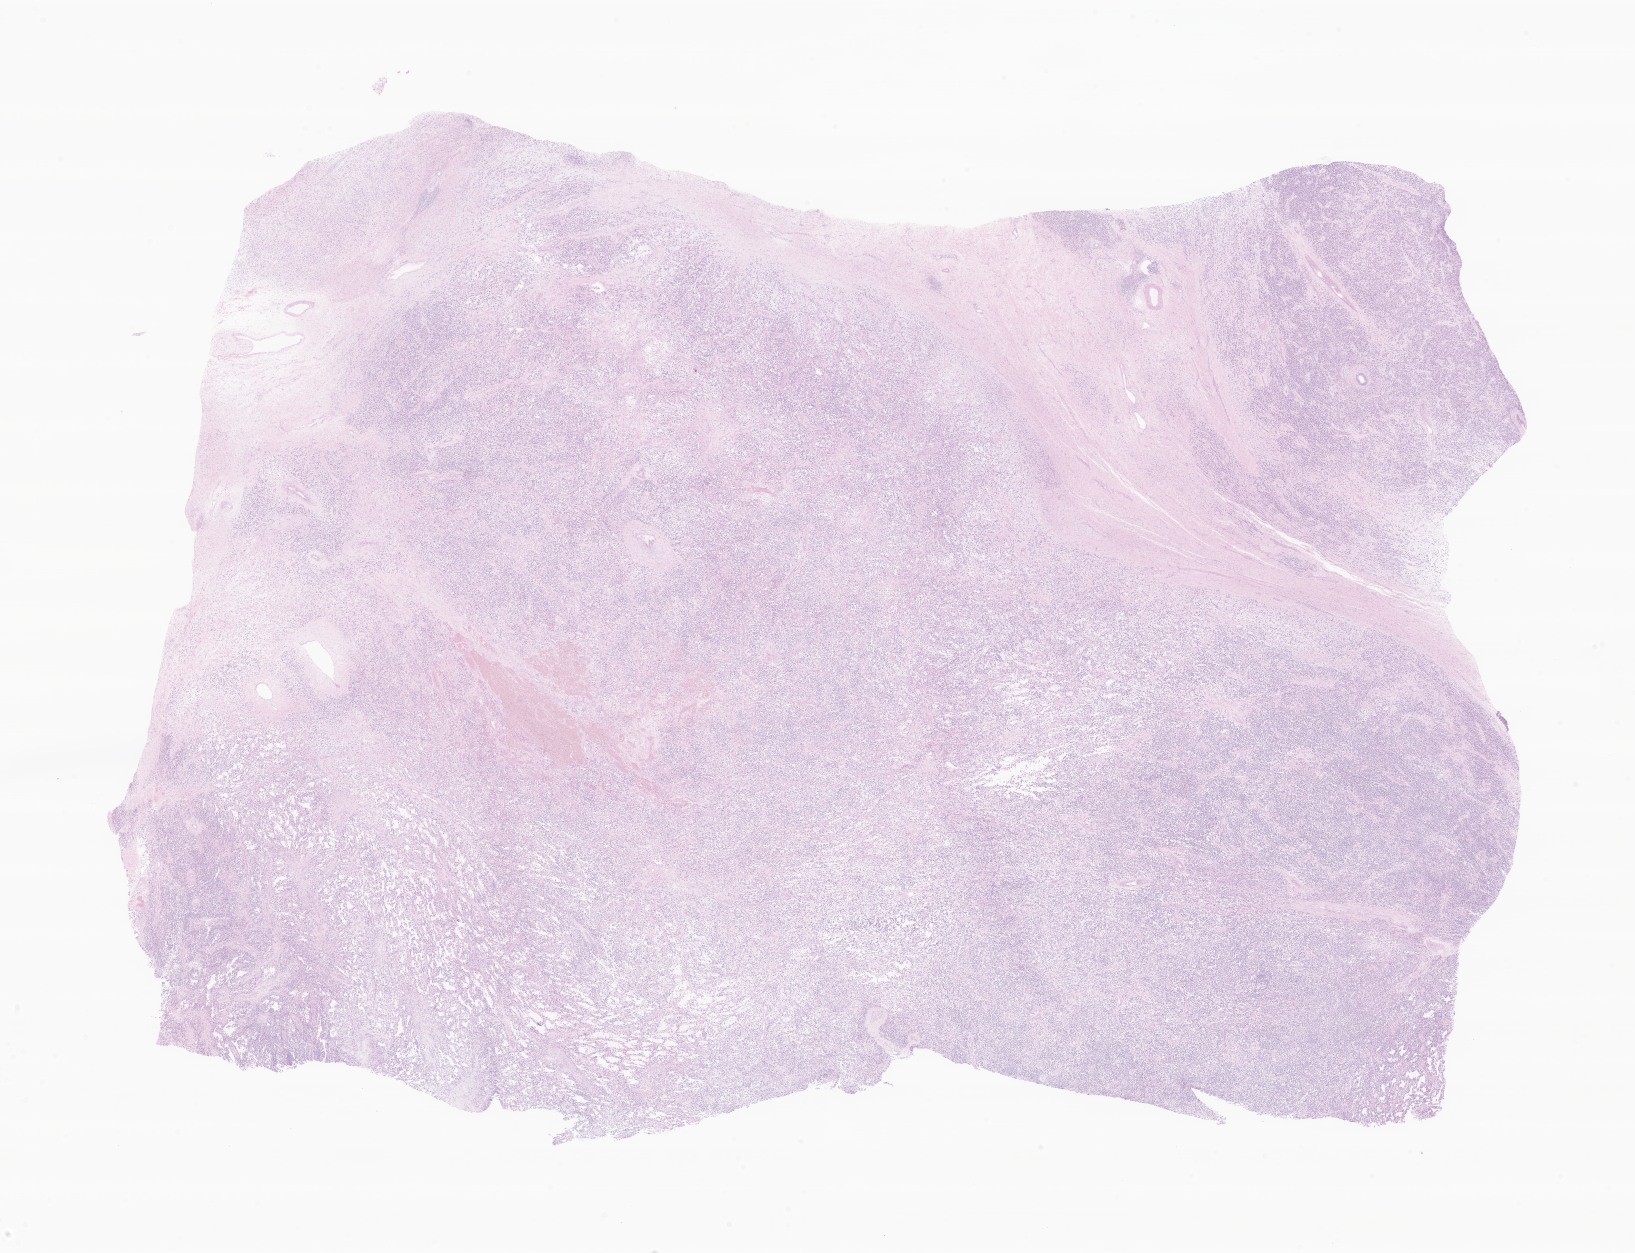
Haematoxylin and eosin whole-slide image of tumor tissue from the testis — a low-resolution overview of the entire scanned area, about 27.6 x 21.1 mm, formalin-fixed, paraffin-embedded (FFPE) tissue. Patient: male, age 196 months (16 years 4 months).
• diagnosis (ICD-O-3 morphology term): Rhabdomyosarcoma, NOS